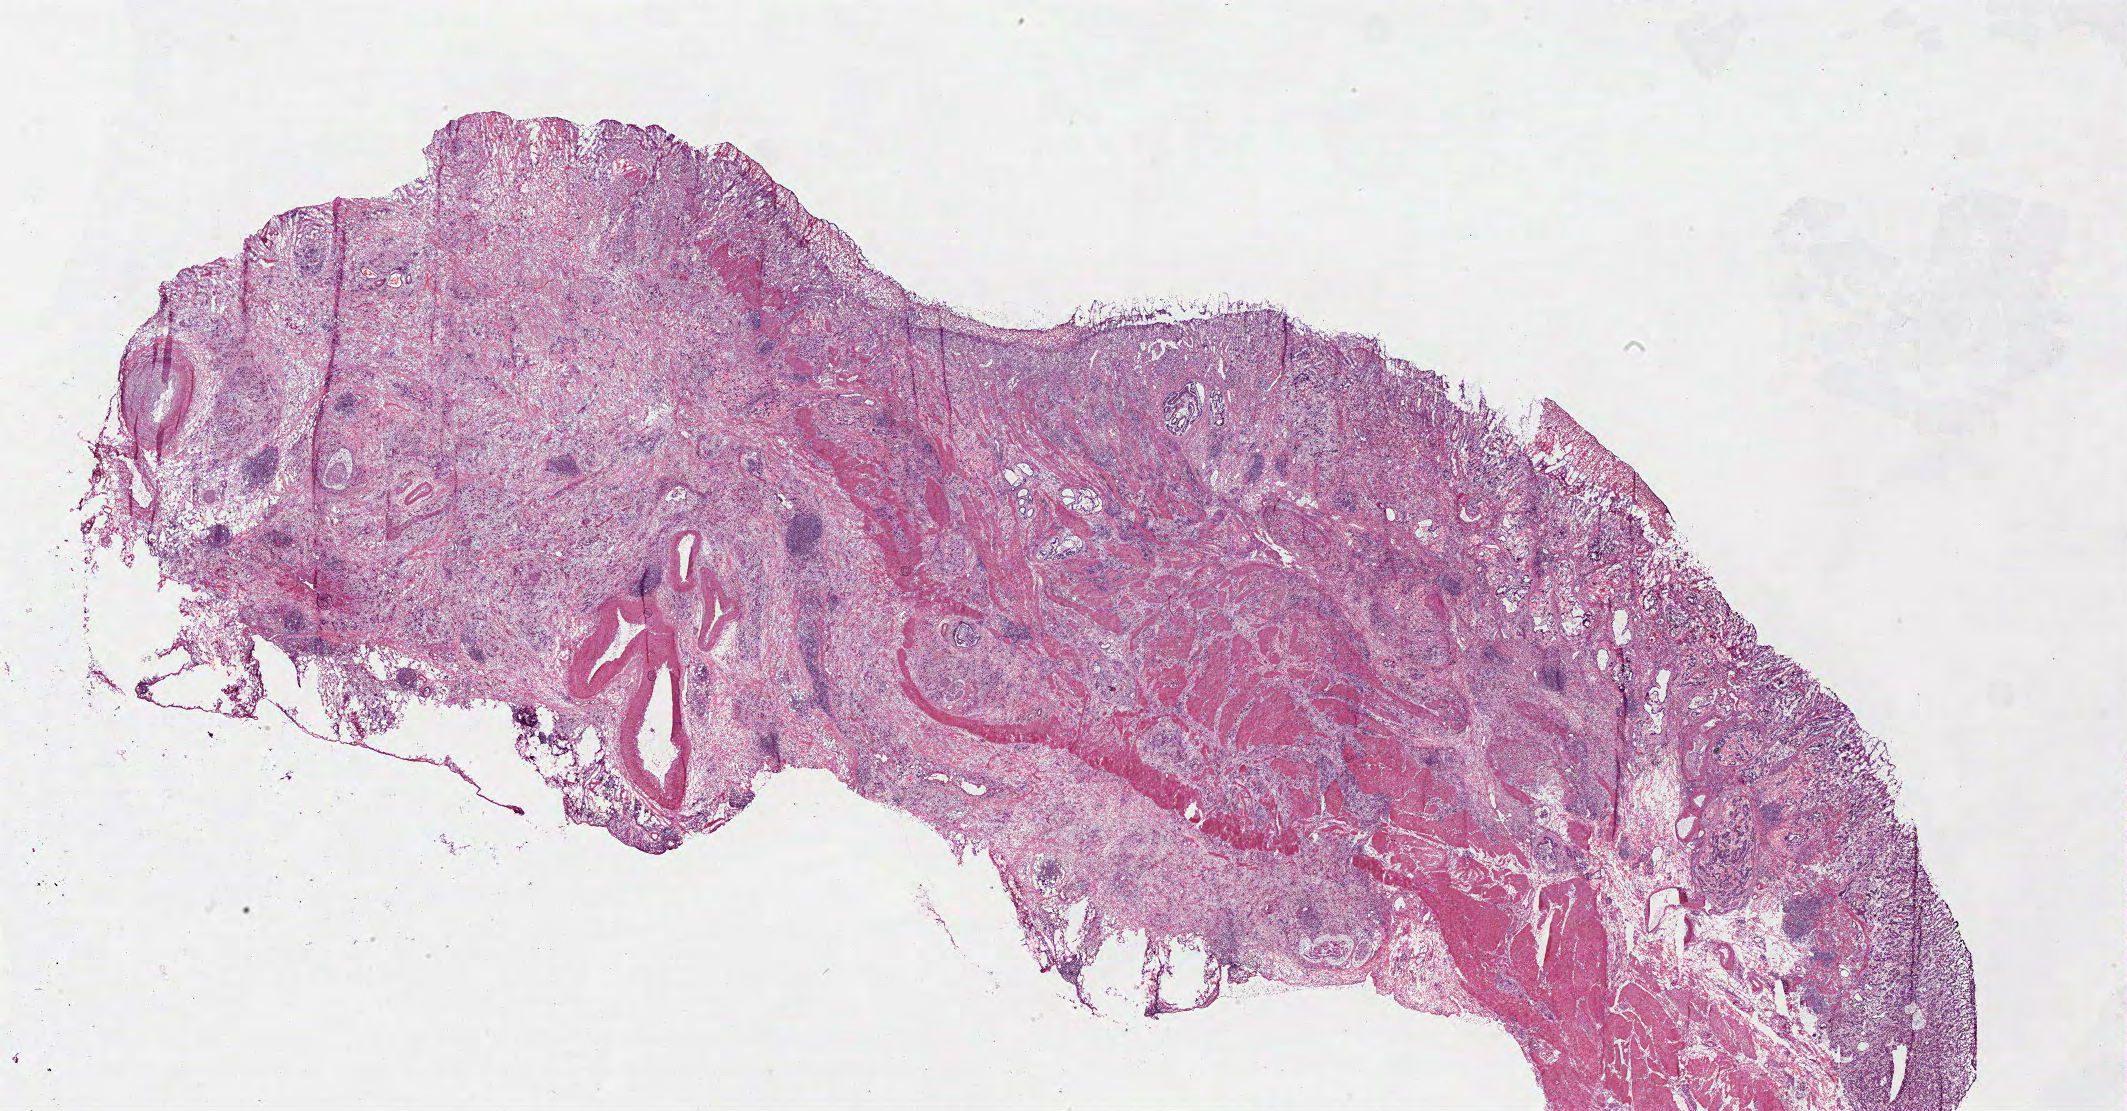
Whole-slide histology image, H&E, whole scanned area (about 33.5 x 17.5 mm, acquisition: 40x scan) shown as a low-resolution overview; frozen section; sample: primary tumour, stomach. Male patient; age at initial diagnosis 69 years. Histologic grade: G3 (poorly differentiated). Slide review estimates, as recorded: tumour cells 85%, tumour nuclei 60%, normal cells 15%, stromal cells 0%, necrosis 0%. Inflammatory infiltration, as recorded: lymphocyte infiltration 15%, monocyte infiltration 0%, neutrophil infiltration 2%.
Lymph nodes positive (case pathology): 0 of 15 examined. Histologic diagnosis: Adenocarcinoma, NOS (body of stomach). AJCC pathologic stage: IIA (7th edition).